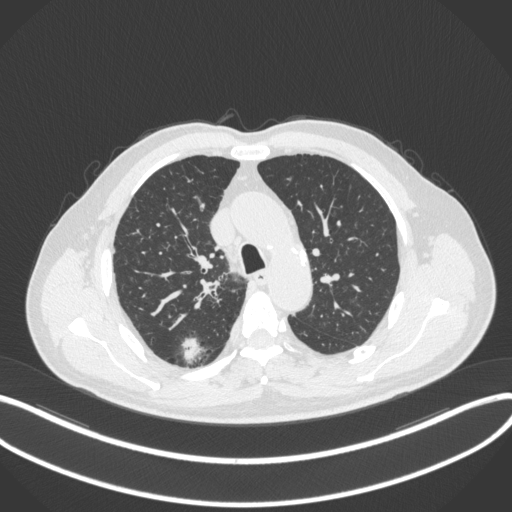
Chest CT, one axial slice; slice 267 of 366 in the series (ordered by position); reconstruction kernel B31f; lung window (W 1500 / L -600 HU); 1 mm slice thickness; 512 × 512 image matrix. Patient: male, 69 years. Case-level facts recorded for this patient, not image findings: clinical TNM (as recorded): T1b N0 M0.
Structures marked on this image (bounding box drawn by a radiologist):
- lung tumour (recorded histology: adenocarcinoma): bounding box <179,334,203,364> (left, top, right, bottom; pixels)